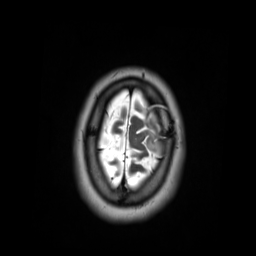
Brain MRI from a brain-tumour surgery series, one axial slice. Slice 50 of 59 in the series (ordered by position). 3.03 mm slice thickness. 256 × 256 image matrix, field of view 250 × 250 mm. From the clinical record (not read from this slice): histopathology: Oligodendroglioma; WHO grade: 2; IDH mutation: yes.
Outlined on this slice (expert manual segmentation):
- tumour: bounding box (x1, y1, x2, y2) in pixels: (139, 133, 177, 158)